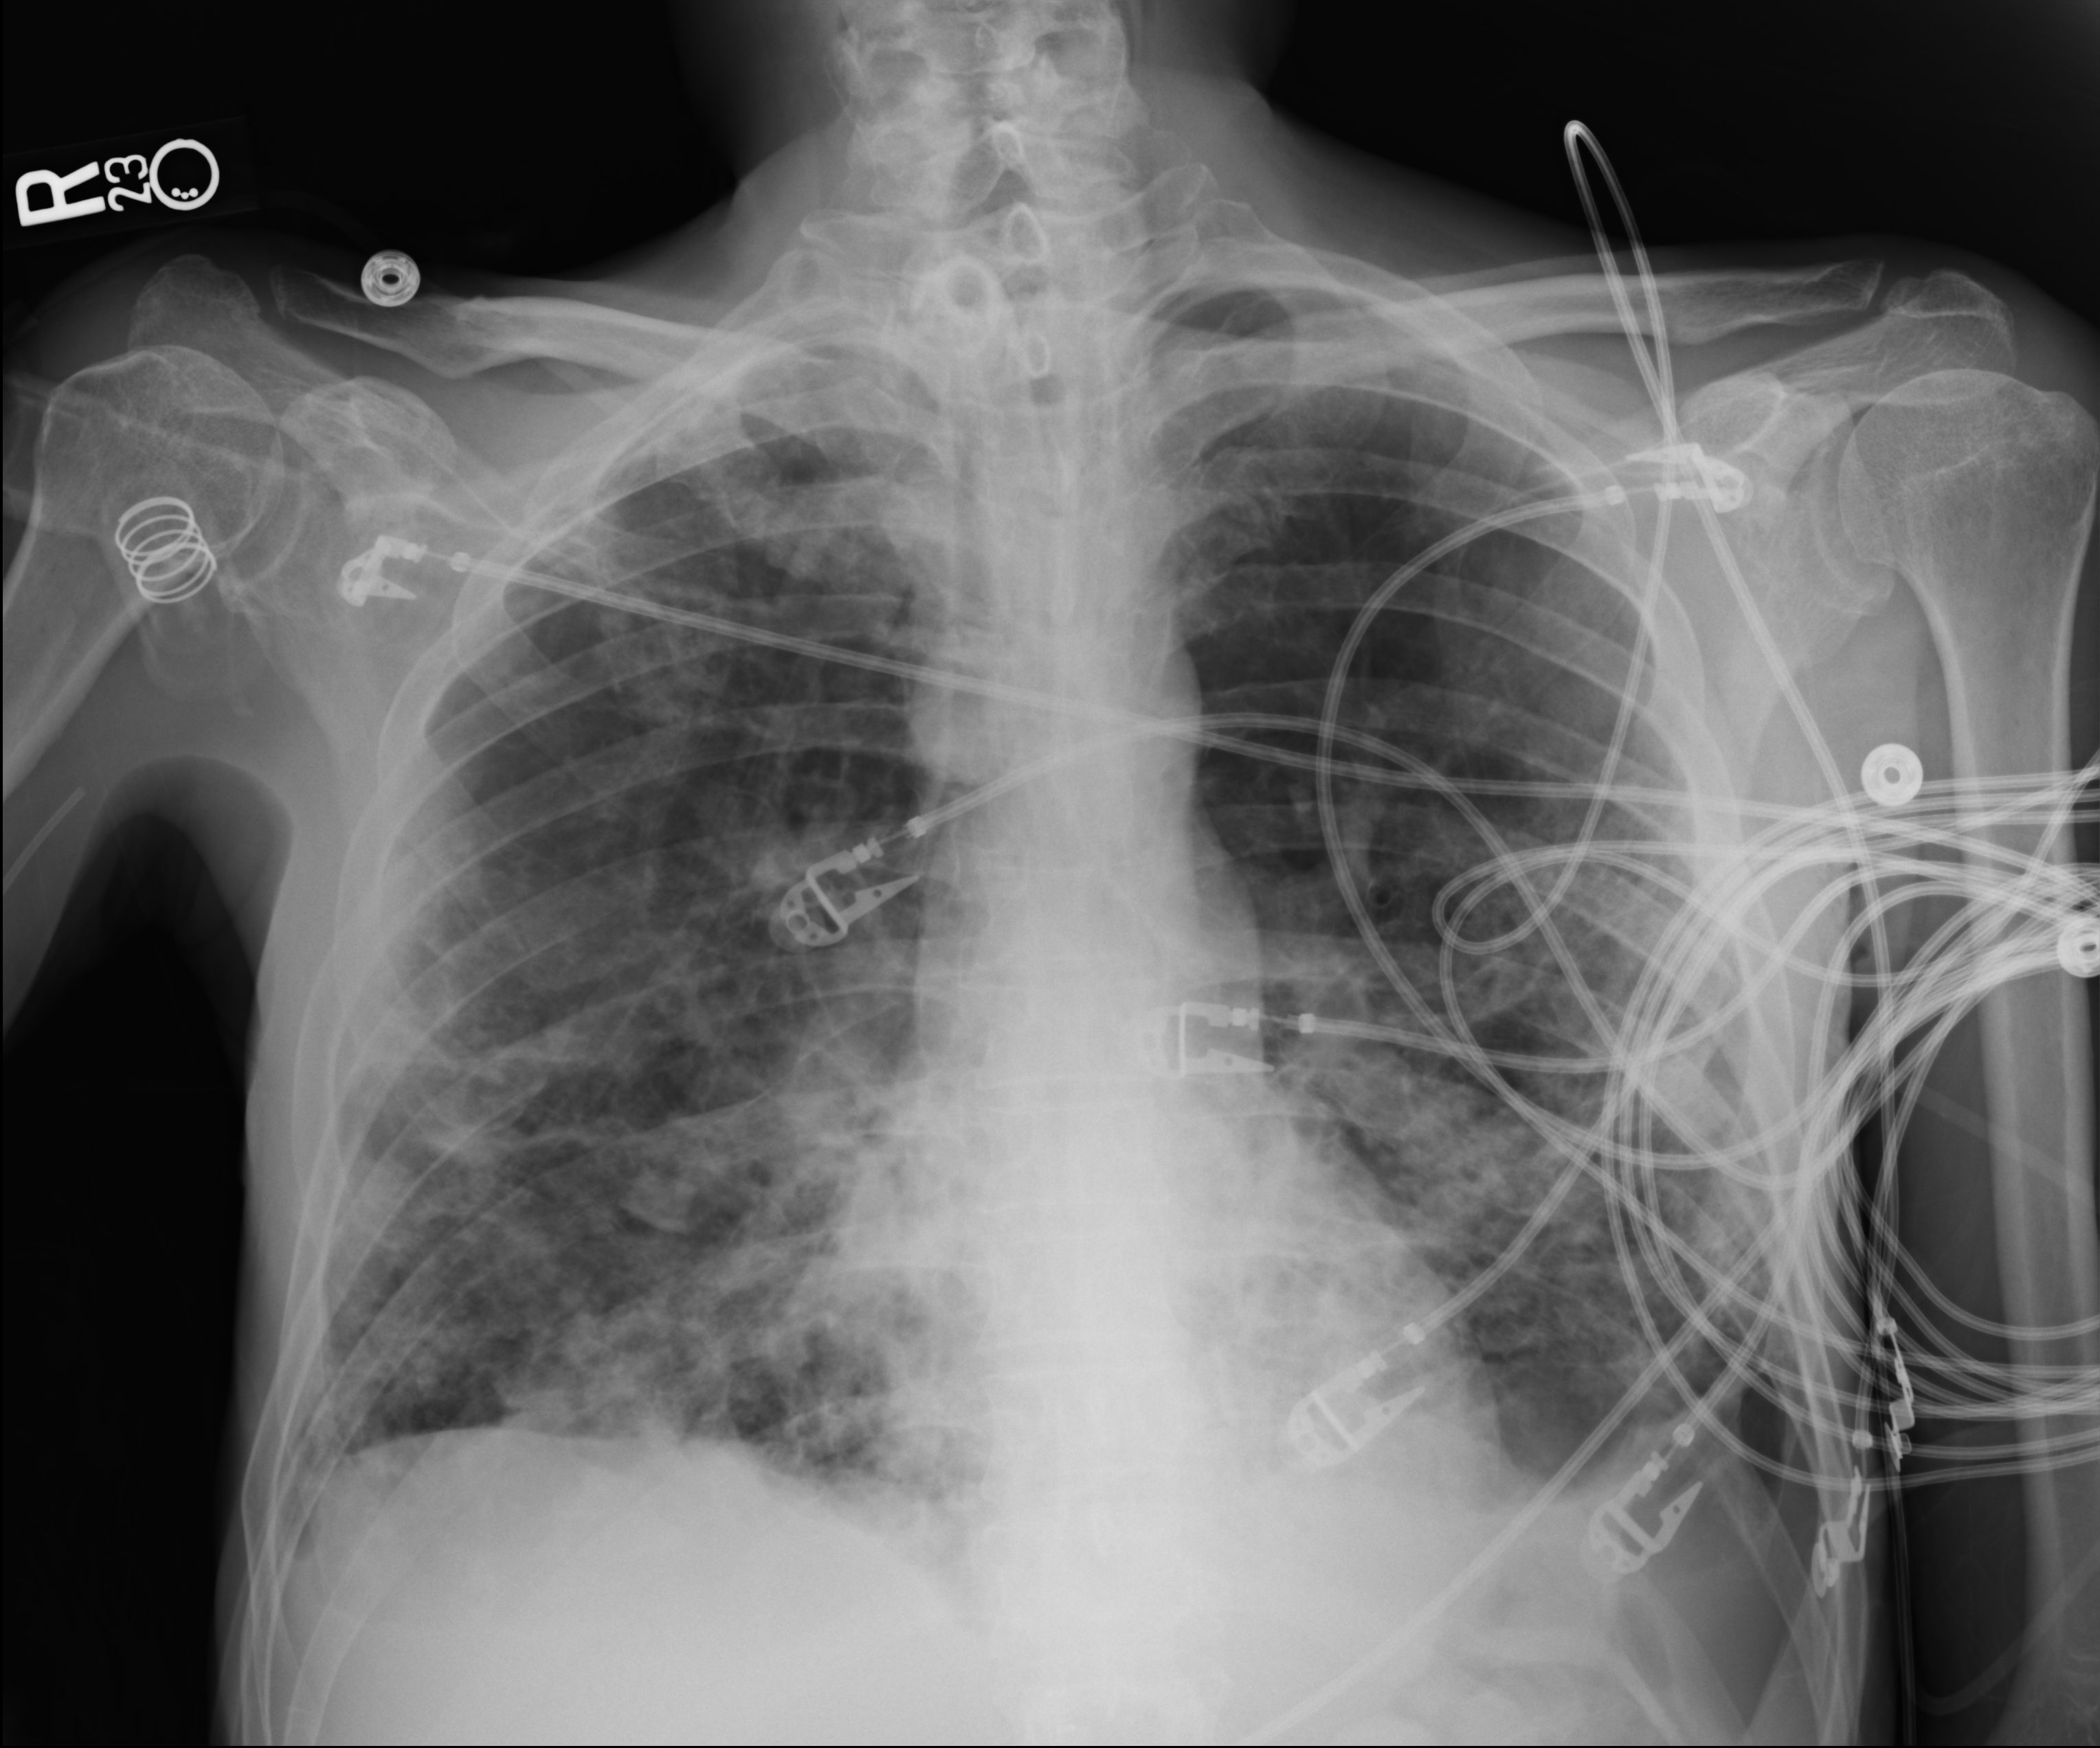
Portable chest radiograph. Patient hospitalised with COVID-19; male, aged 18–59 years.
Hospital-stay facts (about this admission, not read from this image; timing relative to this image not recorded): mechanically ventilated during this hospital stay: yes.